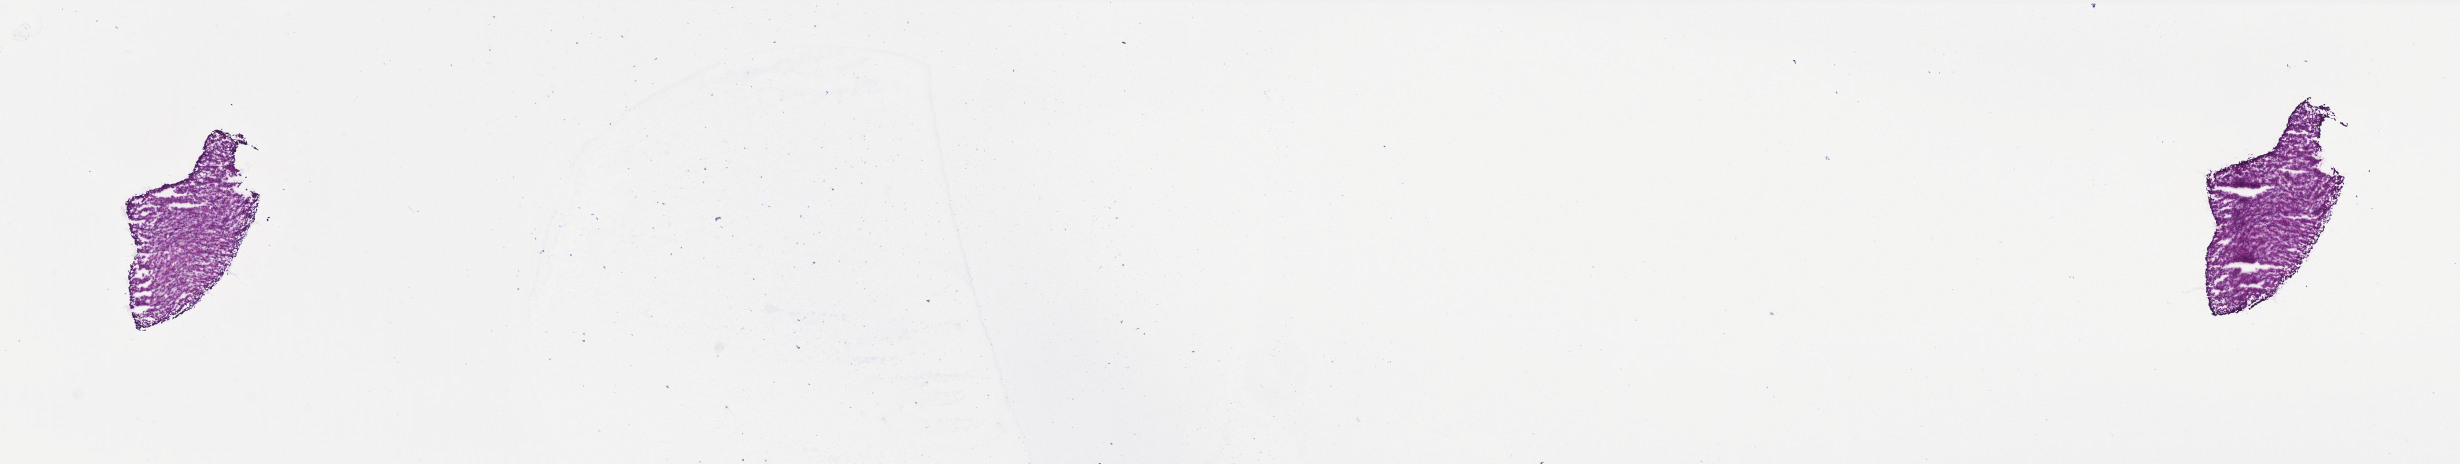
Digitized H&E tissue section (whole slide) — whole scanned area (about 19.7 x 3.7 mm) shown as a low-resolution overview. Frozen section from the top of the tissue portion. Sample: primary tumour, uvea. Female patient; age at initial diagnosis 35 years. Pathologist review of this section (percent, as recorded): tumour cells 100%, tumour nuclei 96%, normal cells 0%, stromal cells 0%, necrosis 0%. Inflammatory infiltration, as recorded: lymphocyte infiltration 0%, monocyte infiltration 0%, neutrophil infiltration 0%.
* histologic diagnosis: Mixed epithelioid and spindle cell melanoma (overlapping lesion of eye and adnexa)
* AJCC pathologic stage: IIIB (7th edition)